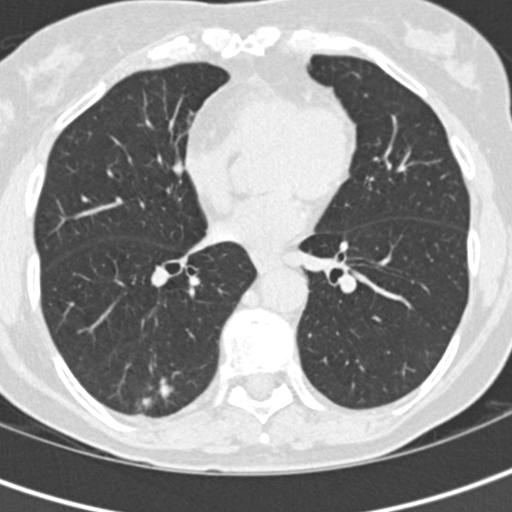
Low-dose screening chest CT, one axial slice. Position 66 of 152 along the scan axis. Reconstruction kernel B30f. 120 kVp. Lung window (W 1500 / L -600 HU). 512 × 512 image matrix, field of view 280 × 280 mm.
Structures marked on this image (manually delineated by an expert):
- lesion 1 (tumor, lower lobe of right lung): bounding box [x1, y1, x2, y2] px = [142, 378, 173, 408]